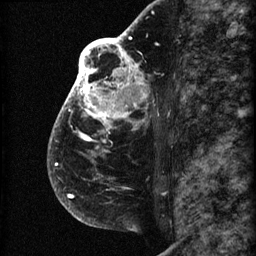
Breast MRI (dynamic contrast-enhanced), one sagittal slice. Position 44 of 60 along the scan axis. 3 images stored at this slice position (order not interpretable as contrast timing). 1.5 T. TE 4.2 ms, TR 22.7 ms. 2 mm slice thickness. 256 × 256 image matrix. Female patient, age 48 years. From the clinical record (not read from this slice): setting: breast cancer imaged before/during neoadjuvant chemotherapy; receptor status: triple-negative.
Annotated regions visible in this slice (semi-automatically segmented with operator editing):
- analysis volume of interest (the breast-tissue region the enhancement analysis was run in; not a lesion): bounding box [x1, y1, x2, y2] px = [47, 30, 173, 207]
- tumour enhancement mask (voxels above the 90 % enhancement threshold inside the analysis volume of interest): [49, 30, 148, 198]